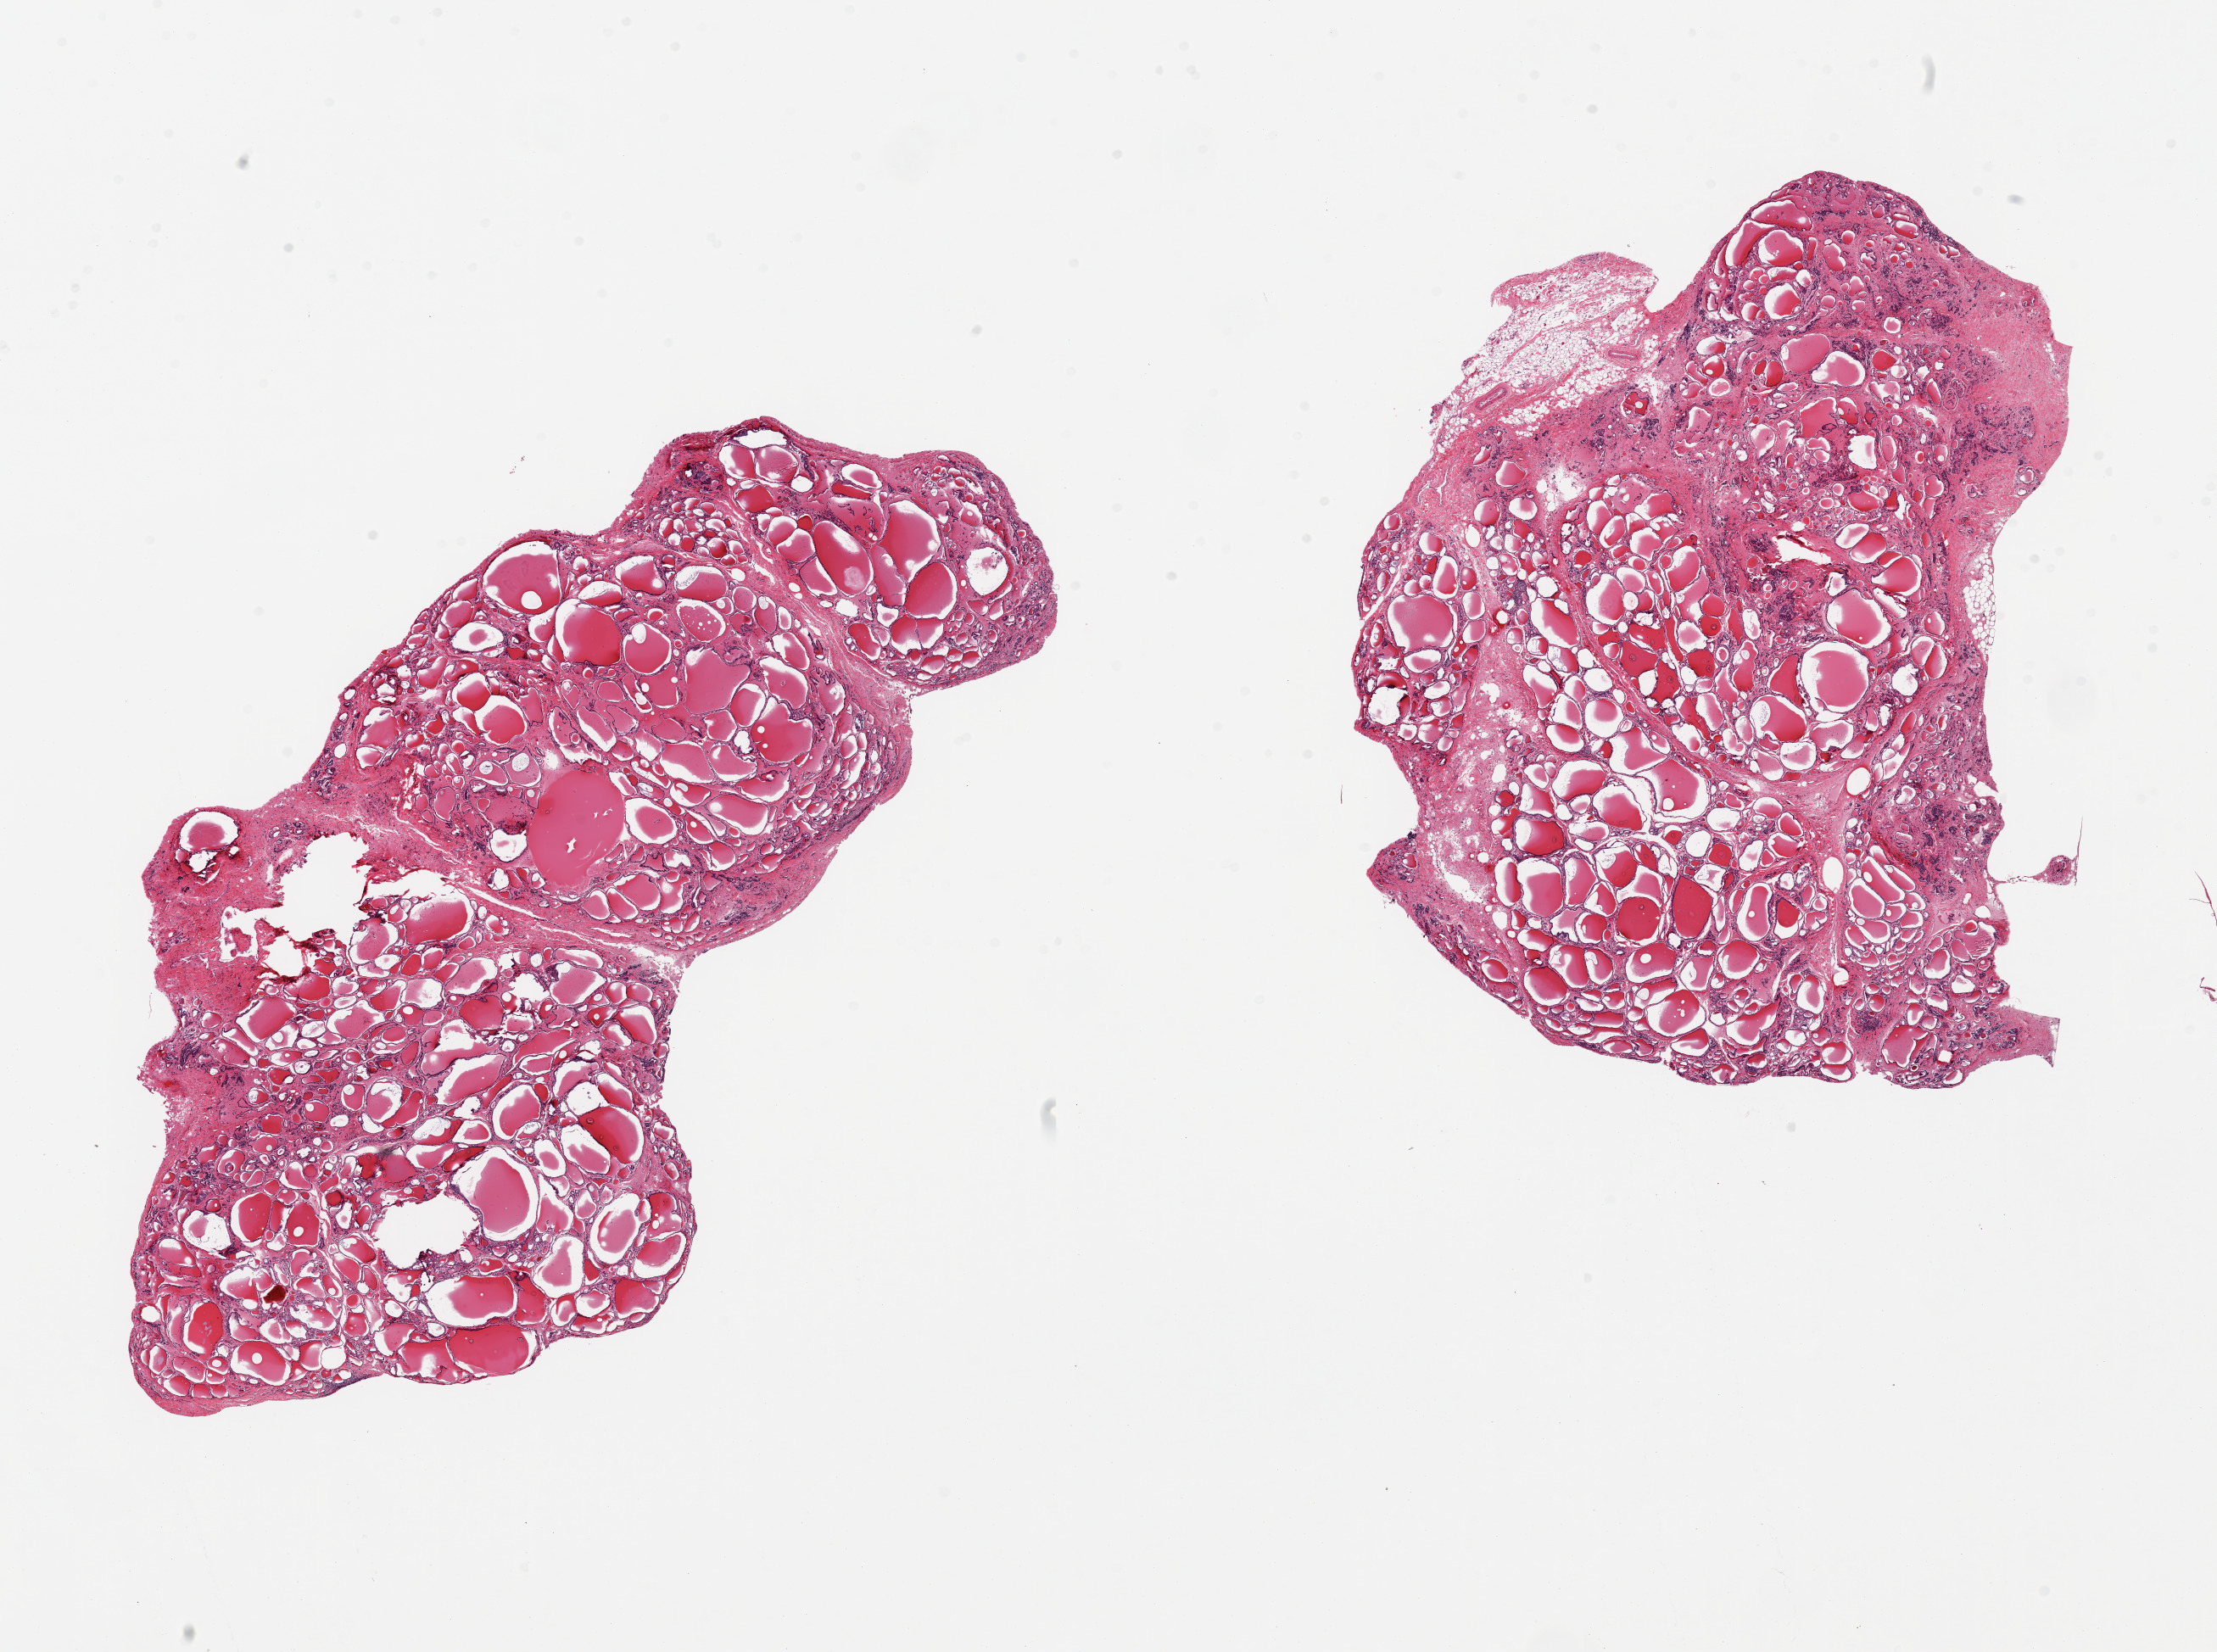
Digitized H&E-stained section, a low-resolution overview of the entire scanned area, about 20.7 x 15.4 mm, PAXgene-fixed paraffin-embedded (PFPE) section, sampled site (target tissue): thyroid, donor tissue sample. Donor: male.
Review note (as recorded): 2 pieces; scattered atrophic areas.